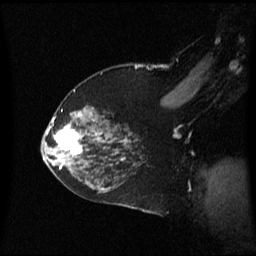
Breast MRI (dynamic contrast-enhanced), one sagittal slice; dynamic contrast-enhanced series, image 2 of 3 at this slice position (ordered by acquisition); 1.5 T; TE 4.2 ms, TR 8.4 ms; 2 mm slice thickness; 256 × 256 image matrix, field of view 240 × 240 mm. Female patient, age 59 years. Case-level facts recorded for this patient, not image findings: setting: breast cancer imaged before/during neoadjuvant chemotherapy; receptor status: HR-positive, HER2-negative.
Outlined on this slice (semi-automatically segmented with operator editing):
- analysis volume of interest (the breast-tissue region the enhancement analysis was run in; not a lesion): bounding box <46,114,89,163> (left, top, right, bottom; pixels)
- tumour enhancement mask (voxels above the 70 % enhancement threshold inside the analysis volume of interest): <55,126,82,155>